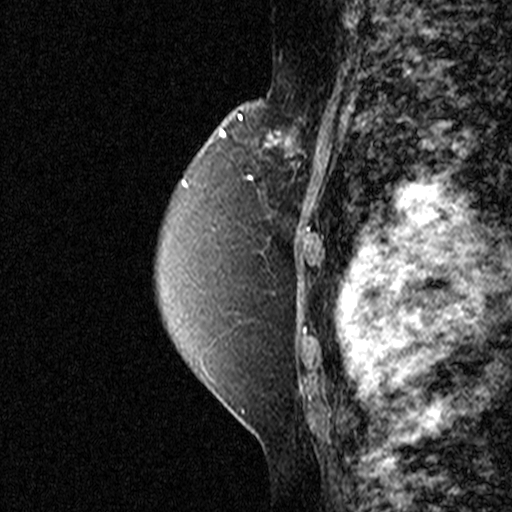
Breast MRI (dynamic contrast-enhanced), one sagittal slice. Slice 31 of 44 in the series (ordered by position). Dynamic contrast-enhanced study with each time point stored as its own series, time point 2 of 3 at this slice position (early post-contrast, ordered by acquisition time). 1.5 T. TE 4.5 ms, TR 11 ms. 512 × 512 image matrix. Patient: female, 49 years. From the clinical record (not read from this slice): setting: breast cancer imaged before/during neoadjuvant chemotherapy; receptor status: triple-negative.
Structures marked on this image (semi-automatic segmentation, software-assisted and operator-edited):
- analysis volume of interest (the breast-tissue region the enhancement analysis was run in; not a lesion): bounding box <250,100,335,197> (left, top, right, bottom; pixels)
- tumour enhancement mask (voxels above the 90 % enhancement threshold inside the analysis volume of interest): <265,125,307,169>